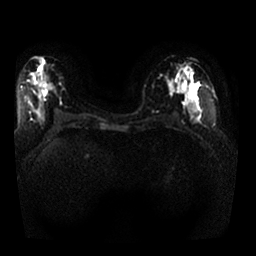
Breast MRI, one axial slice; slice 11 of 25 in the series (ordered by position); diffusion-weighted series; image 2 of 4 stored at this slice position (different b-values; order by instance number); 1.5 T; 256 × 256 image matrix, field of view 350 × 350 mm. Female patient.
Structures marked on this image (manually delineated by an expert):
- tumour on diffusion-weighted imaging: bounding box [x1, y1, x2, y2] px = [183, 80, 187, 90]